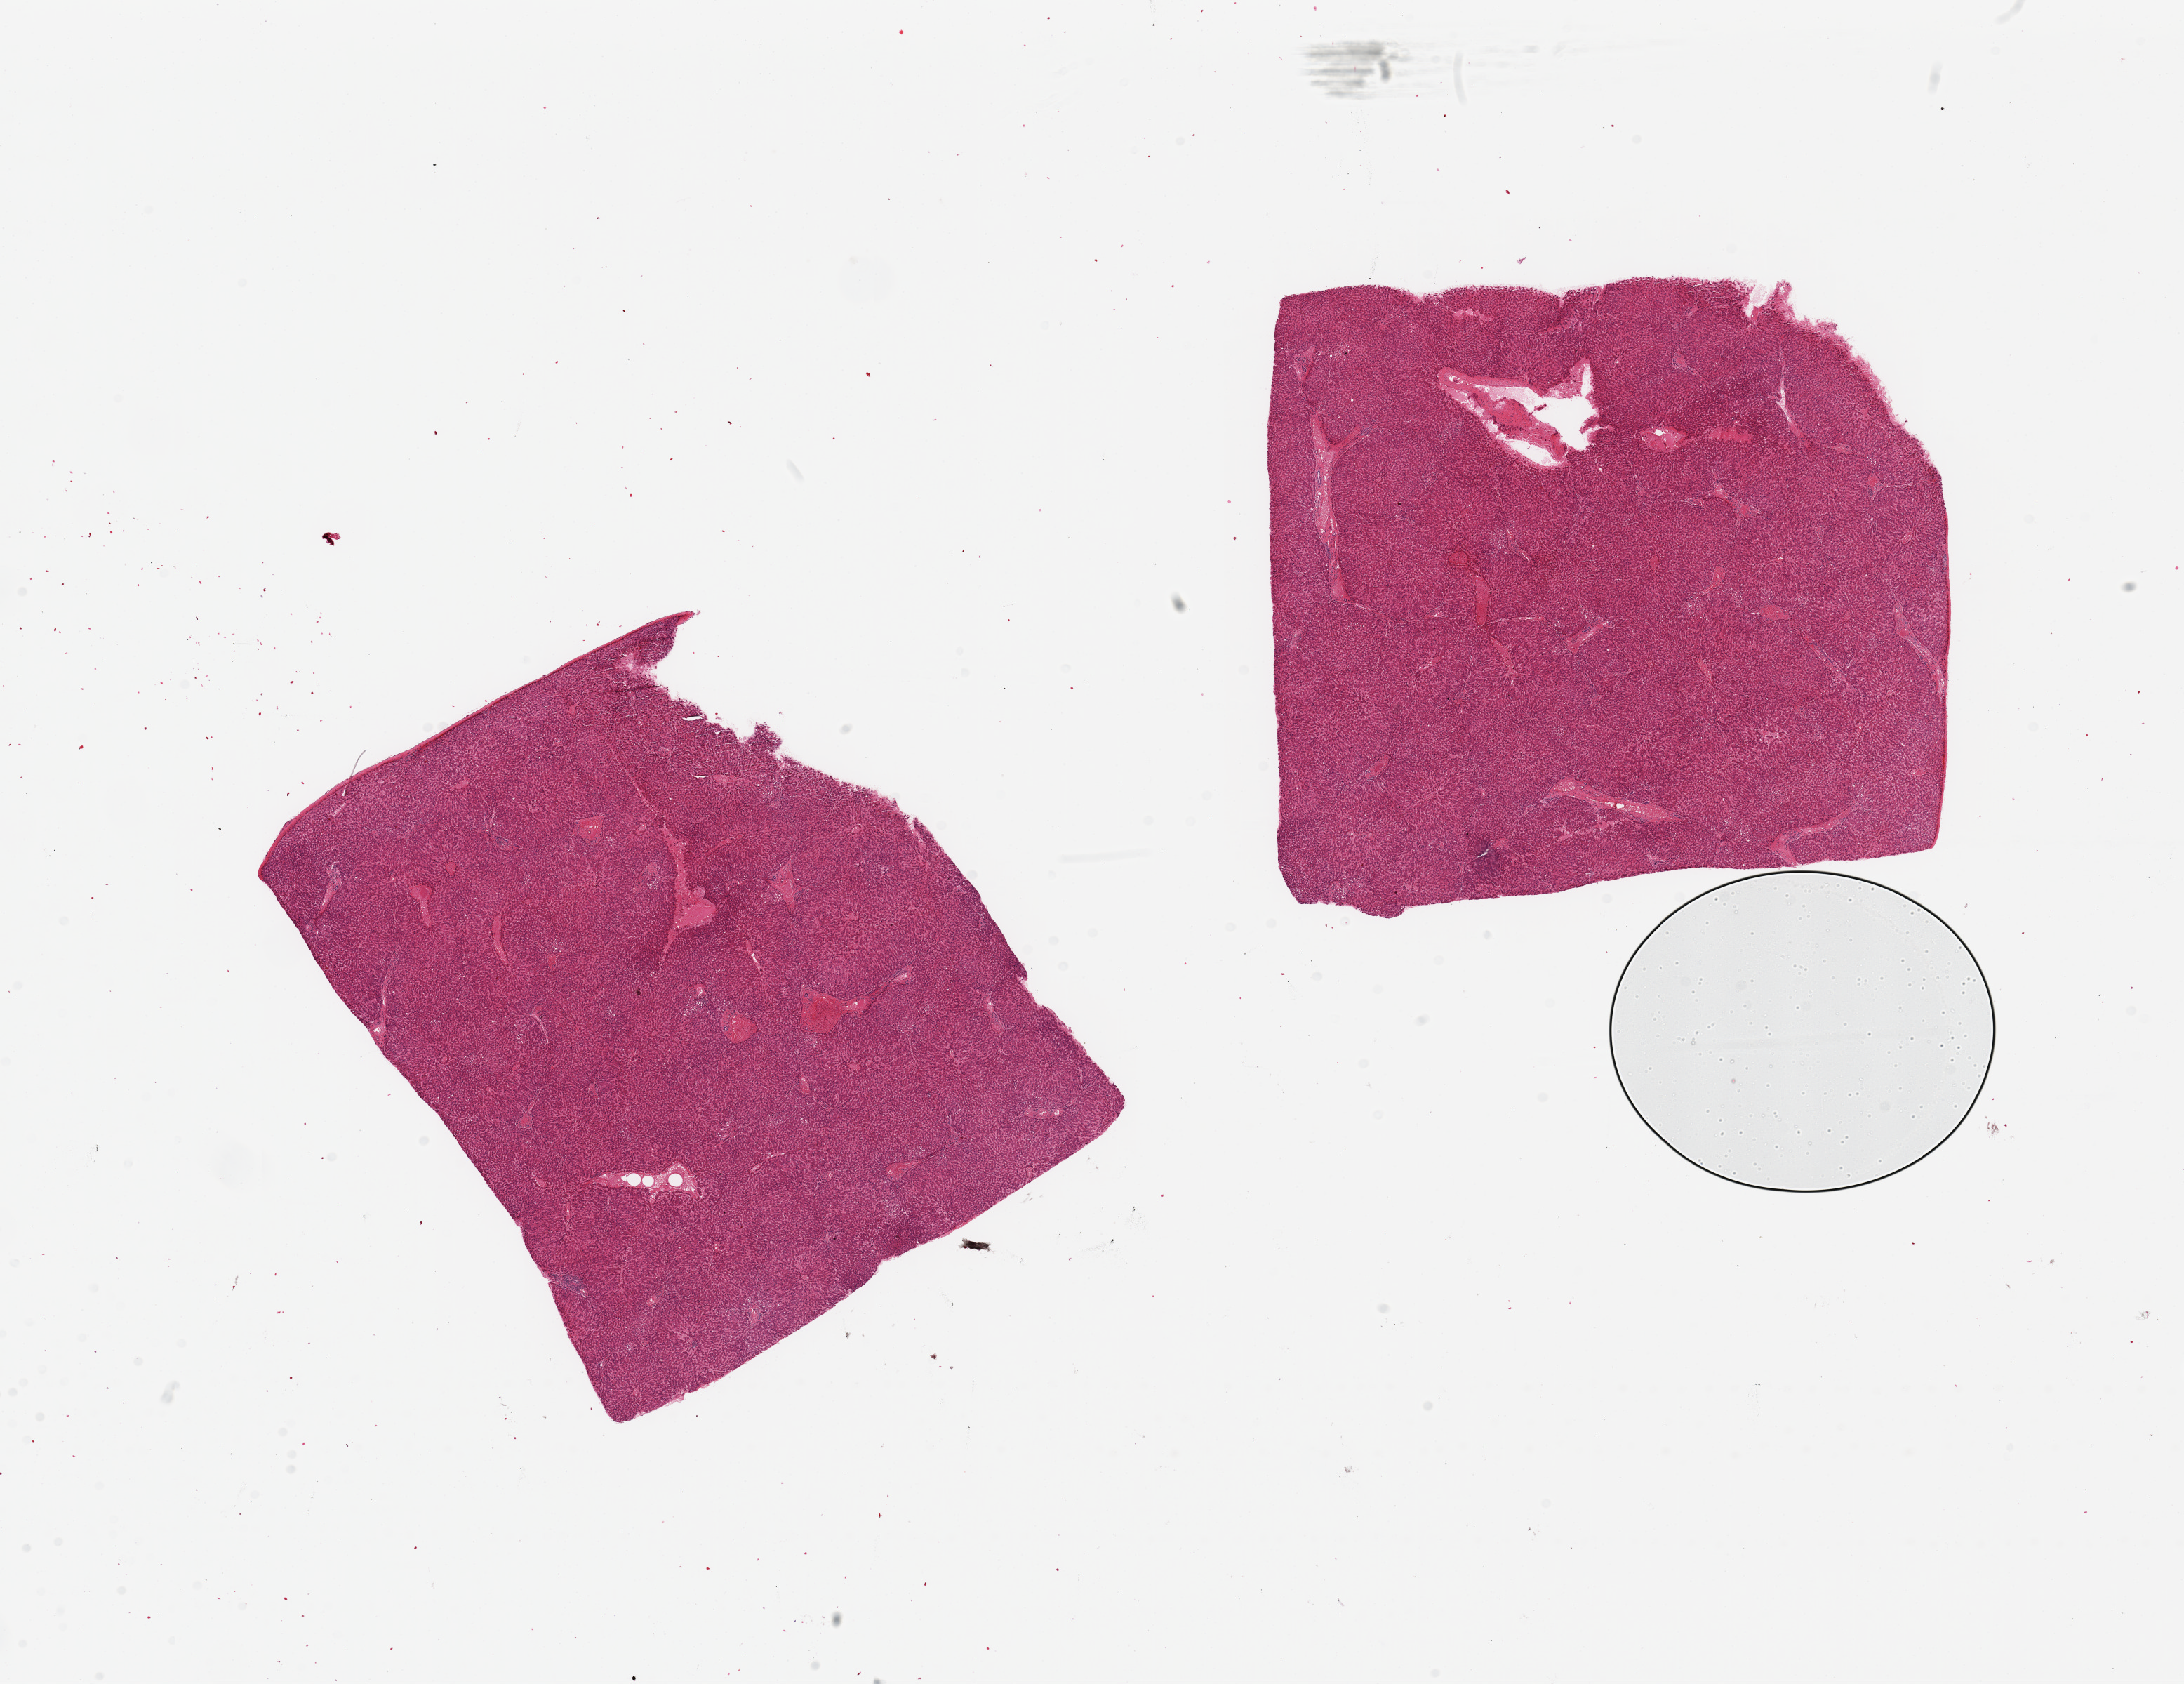
Whole-slide image, hematoxylin and eosin (H&E) stain, low-resolution overview of the scanned area, about 24.6 x 19.0 mm; PAXgene-fixed, paraffin-embedded tissue; section of liver (target tissue); tissue donor sample. Male donor.
Reviewer comment on this tissue sample: 2 pieces, 8x7 & 7.5x7mm; no significant fat.